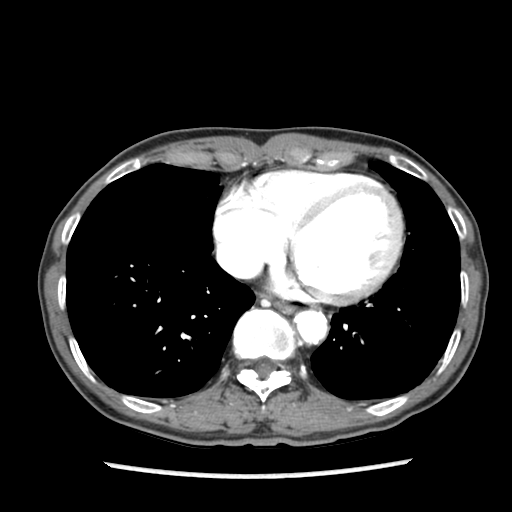
Contrast-enhanced abdominal CT (liver protocol), one axial slice. Slice 83 of 87 in the series (ordered by position). Soft-tissue window (W 400 / L 40 HU). 512 × 512 image matrix, field of view 300 × 300 mm. From the clinical record (not read from this slice): diagnosis: hepatocellular carcinoma (patient treated with transarterial chemoembolisation; whether this scan precedes or follows treatment is not stated here); TNM stage (as recorded): Stage-IIIB; Child-Pugh class: A; tumour differentiation: well differentiated; tumour nodularity: uninodular.
Structures marked on this image (semi-automatically segmented with operator editing):
- abdominal aorta: bounding box [x1, y1, x2, y2] px = [297, 310, 326, 342]